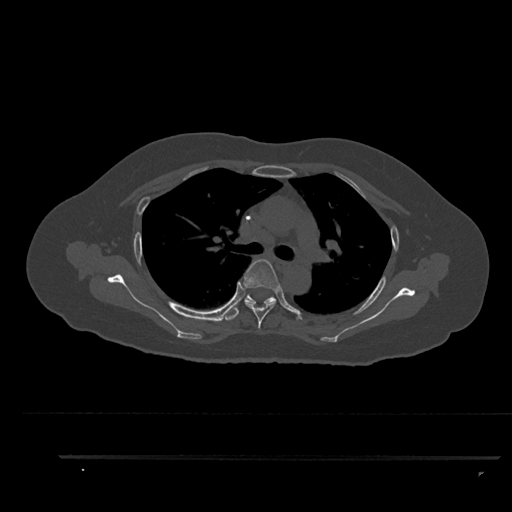
CT including the spine, one axial slice. Slice 626 of 797 in the series (ordered by position). 120 kVp. Bone window (W 1800 / L 400 HU). 0.5 mm slice thickness. 512 × 512 image matrix, field of view 408 × 408 mm. Patient: female, 44 years. From the clinical record (not read from this slice): primary cancer: renal; vertebrae with lytic lesions (as recorded): L1.
Structures marked on this image (semi-automatic segmentation, software-assisted and operator-edited):
- T4 vertebra: bounding box (x1, y1, x2, y2) in pixels: (243, 259, 280, 329)
- T5 vertebra: (225, 294, 276, 321)